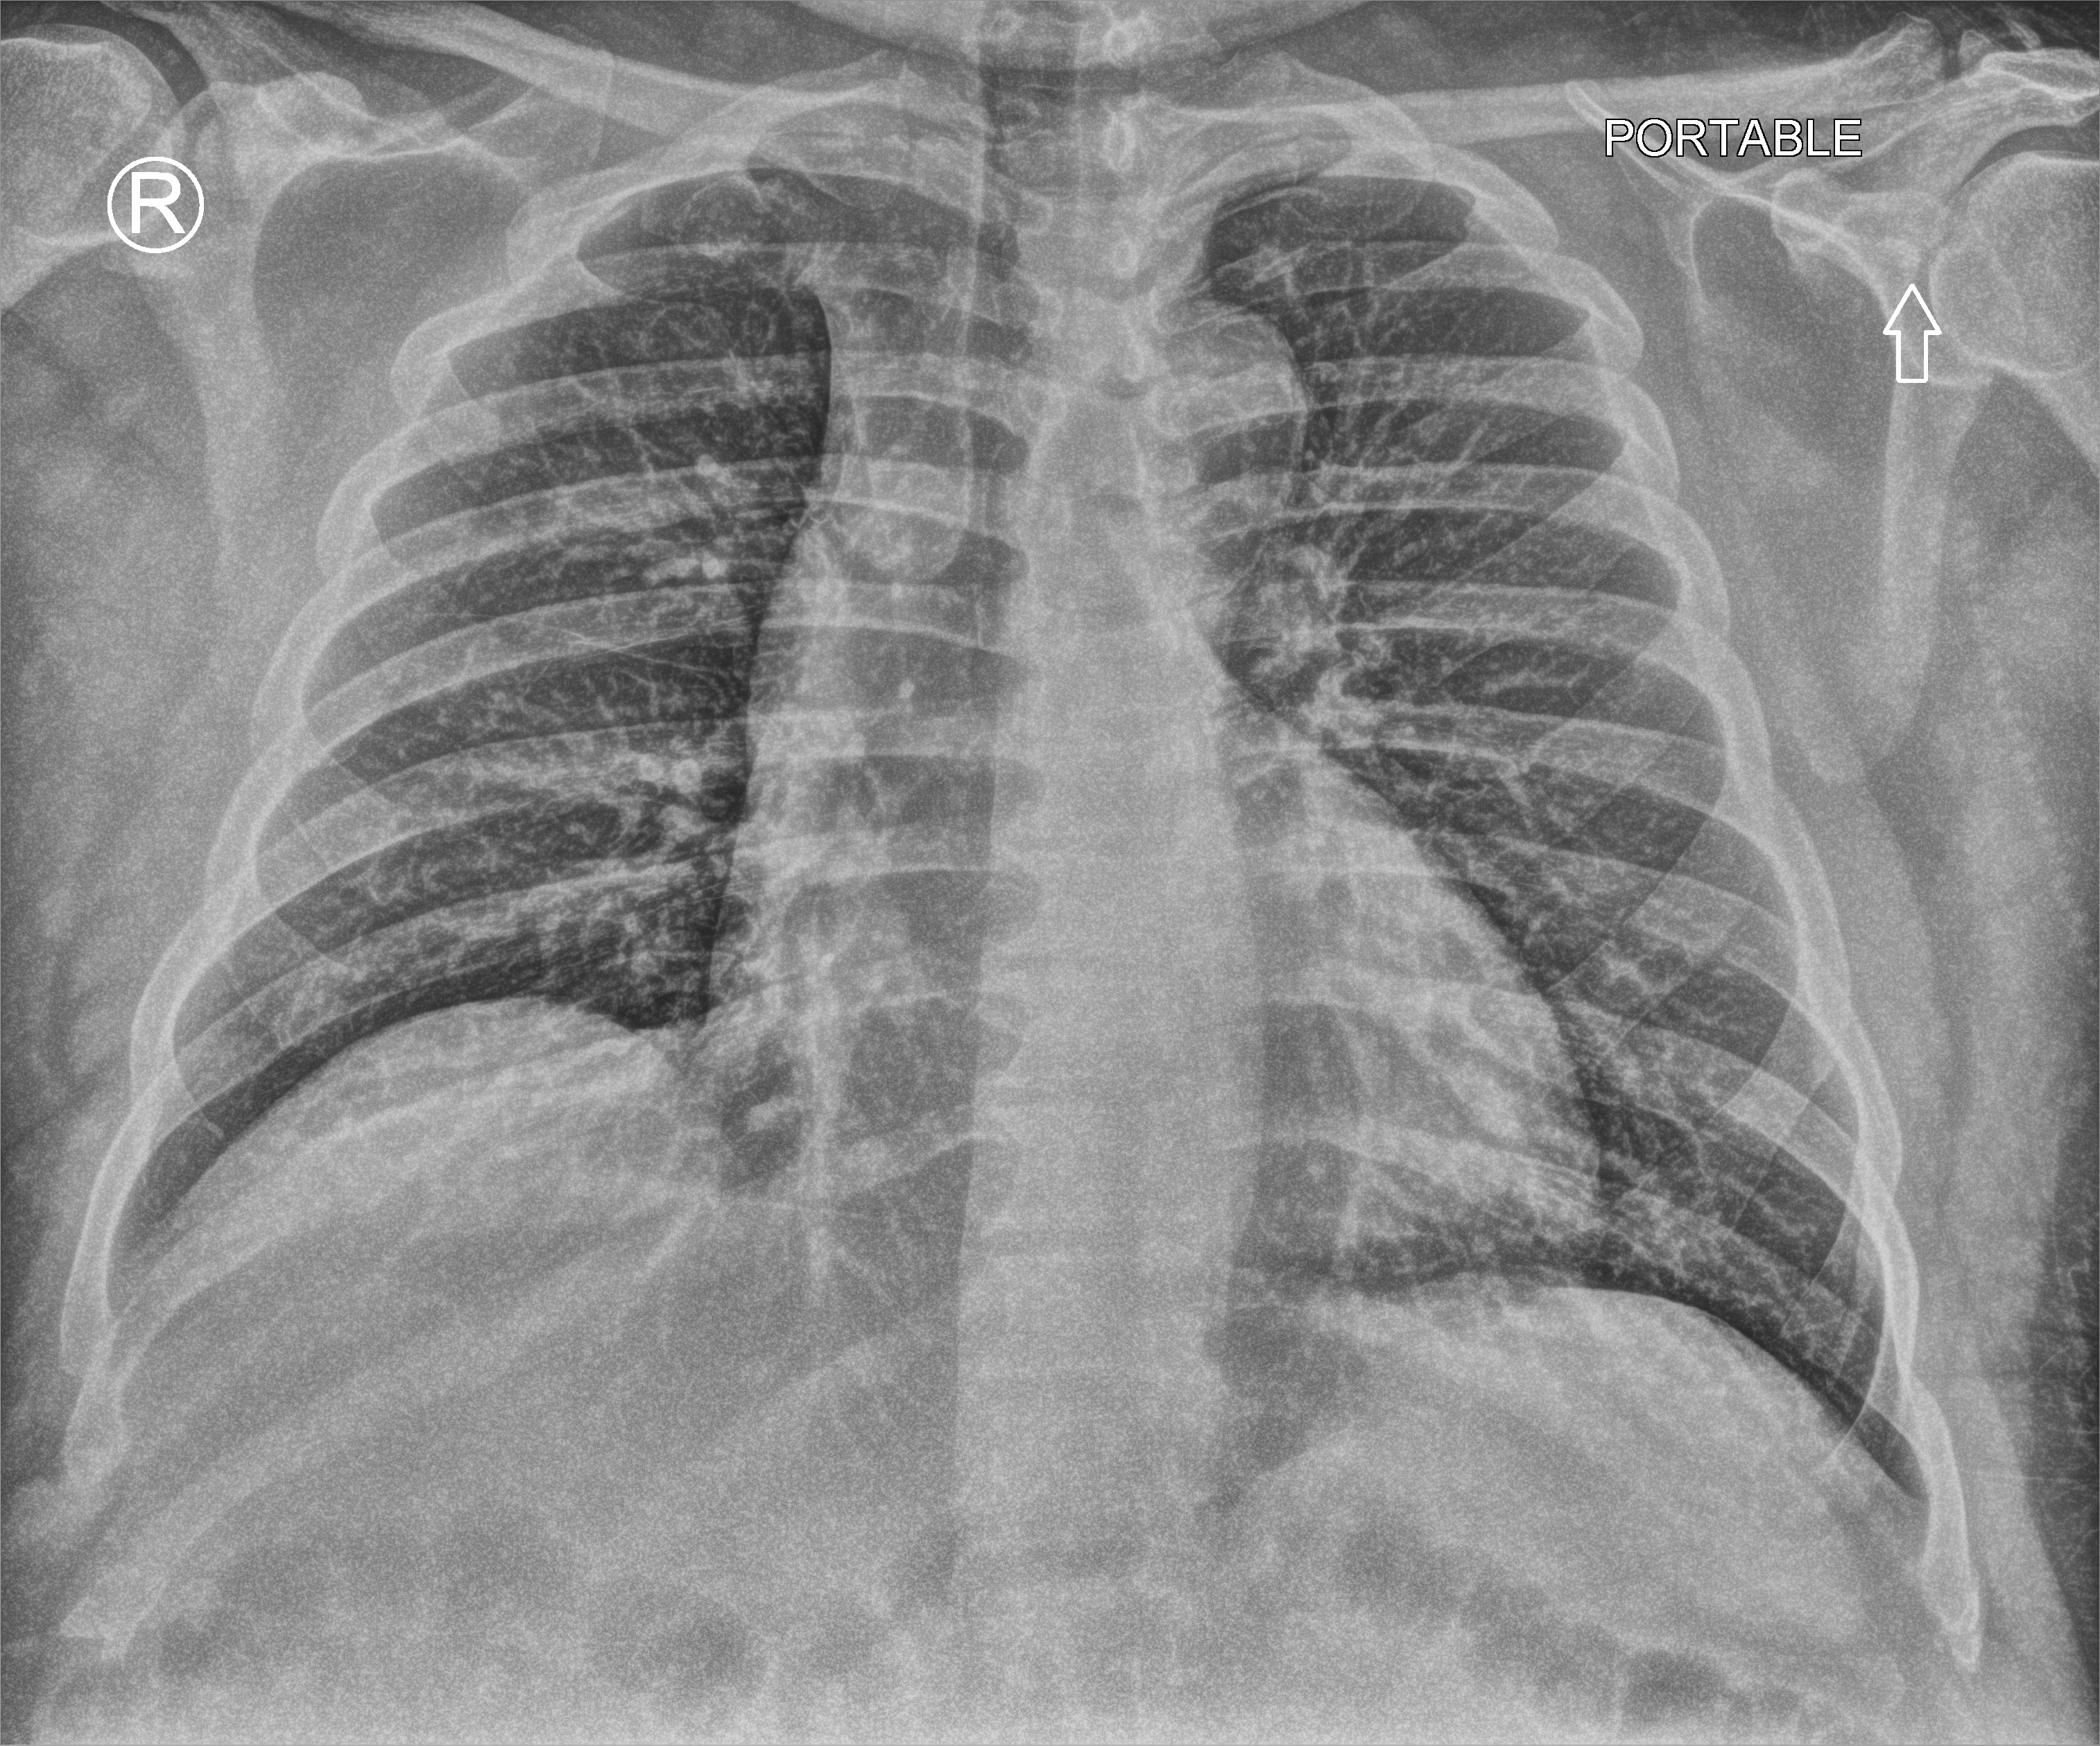
Chest X-ray (portable), anteroposterior (AP) projection. Male patient hospitalised with COVID-19, age 18–59 years.
From the hospital-stay record, not from the radiograph (when in the stay this image was taken is not recorded): chronic kidney disease (admission record): no; COPD (admission record): no; other chronic lung disease (admission record): no.